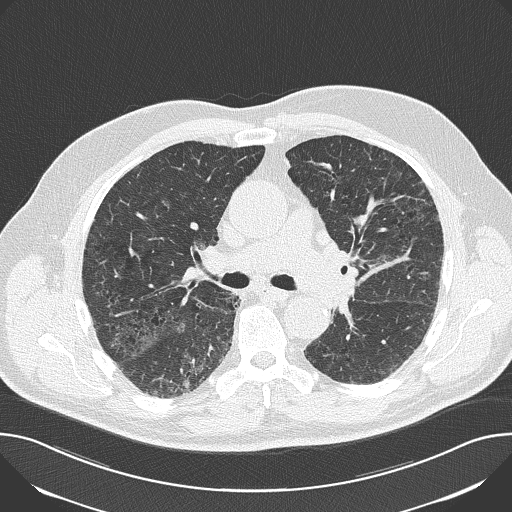
Low-dose screening chest CT, axial slice, baseline annual screen, lung window (W 1500 / L -600 HU), slice 70 of 163 in the series. Male participant, aged 69 years at enrolment. Current smoker at enrolment.
- Expert-annotated lung lesion, bounding box <160,360,206,402> (left, top, right, bottom; pixels).
- No non-calcified nodule or mass ≥4 mm was recorded by the screening reader at this exam.
- Official screen result: negative screen, significant abnormalities not suspicious for lung cancer.
- Lung cancer was diagnosed 658 days after this screen: squamous cell carcinoma, NOS, right lower lobe, moderately differentiated (G2), stage IA (AJCC 6th edition), 25 mm at pathology.